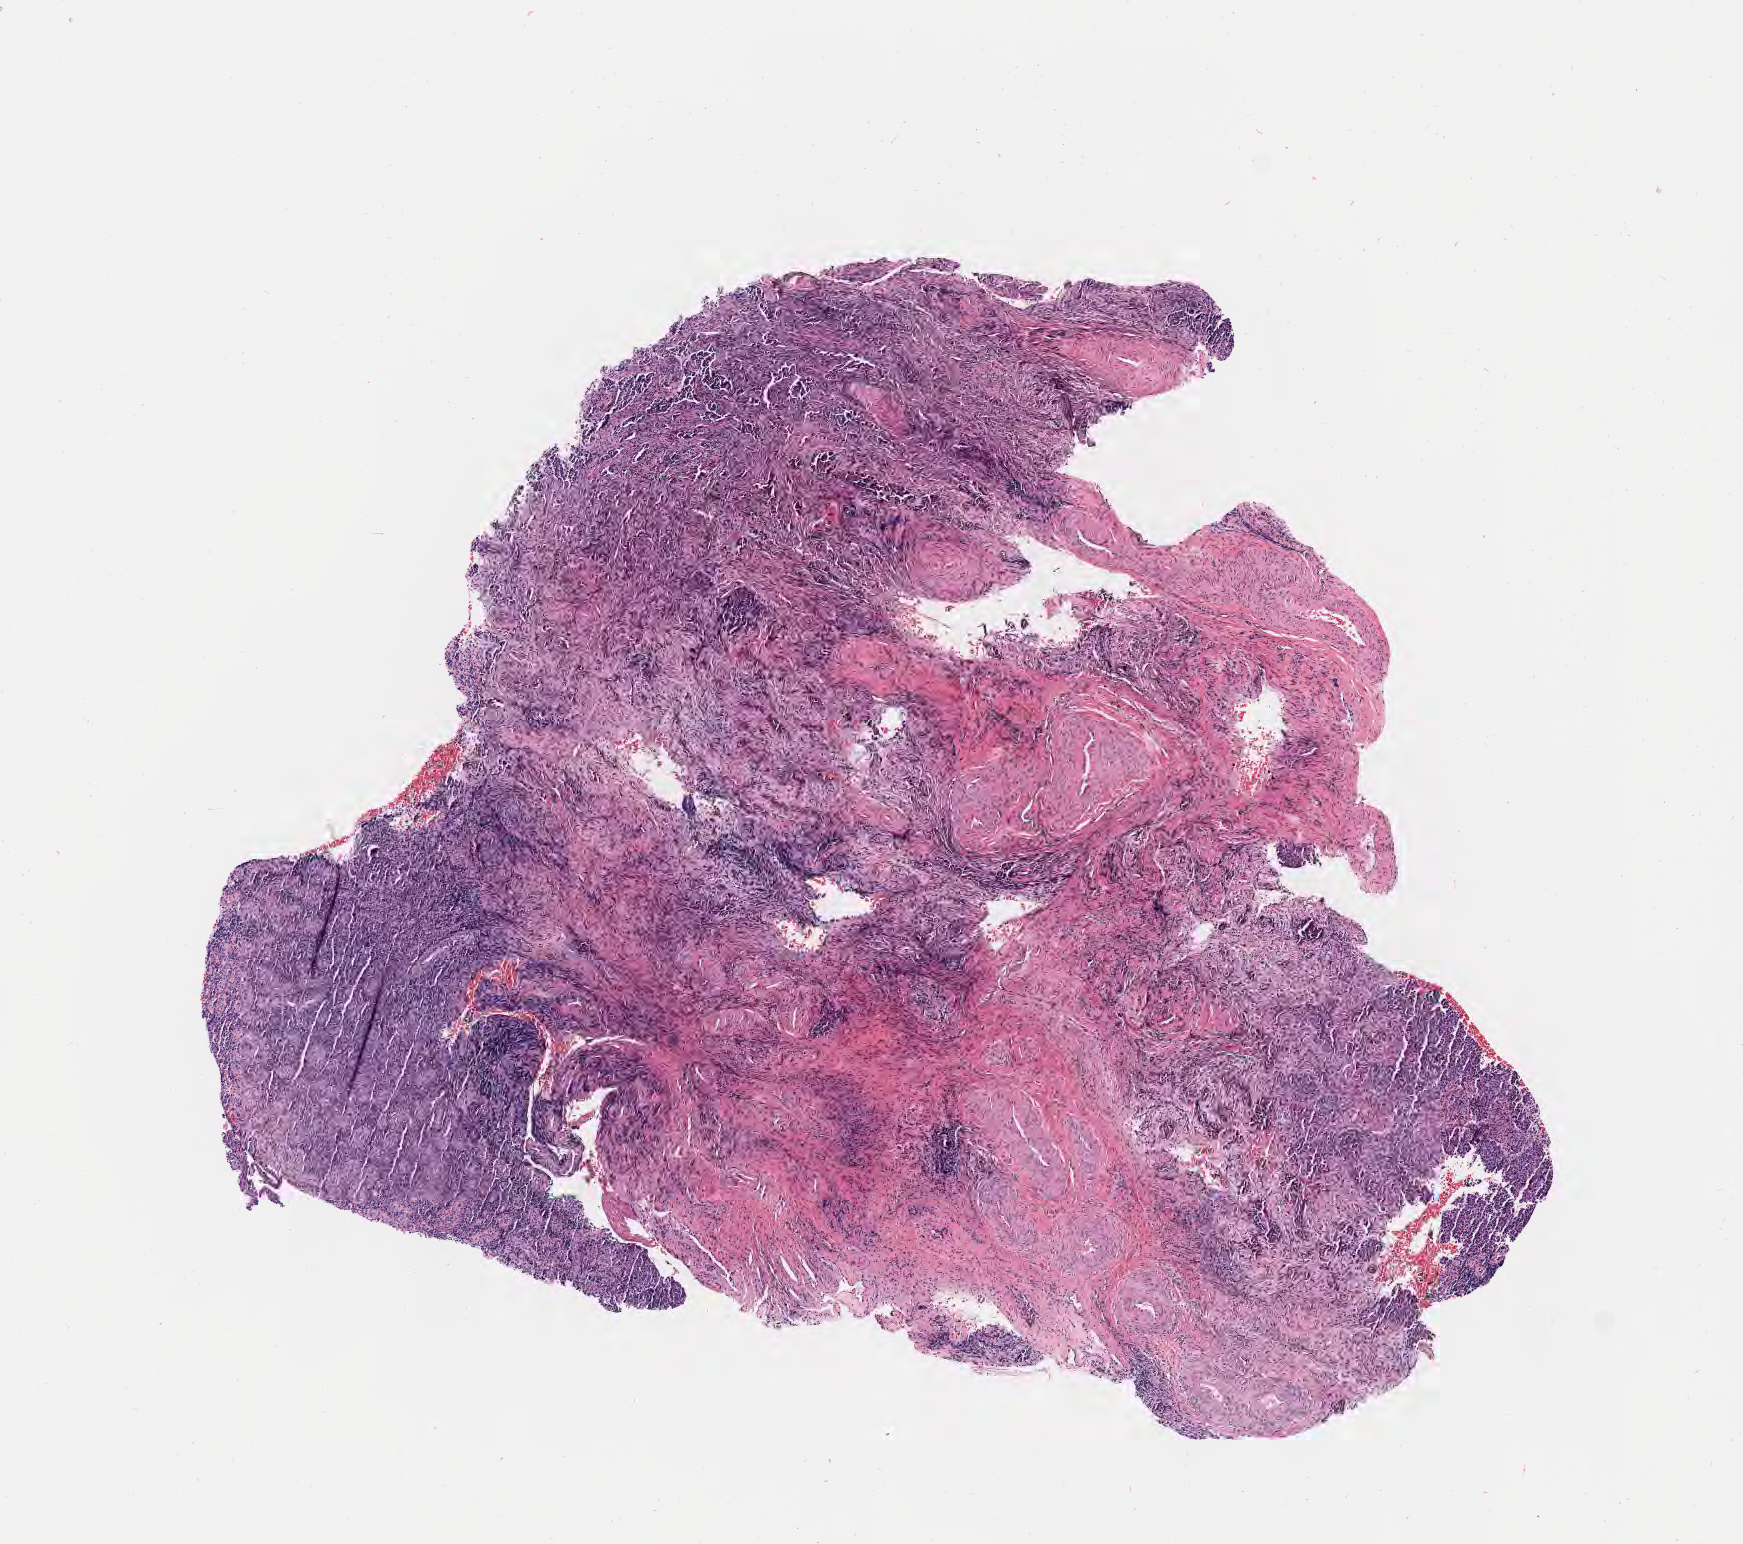
Digitized hematoxylin and eosin (H&E)-stained section — whole scanned area (about 7.0 x 6.2 mm) shown as a low-resolution overview. Specimen: tumor tissue. Site: cervix. Patient female; age 31 years.
Diagnosis: Squamous cell carcinoma, large cell, nonkeratinizing, NOS.